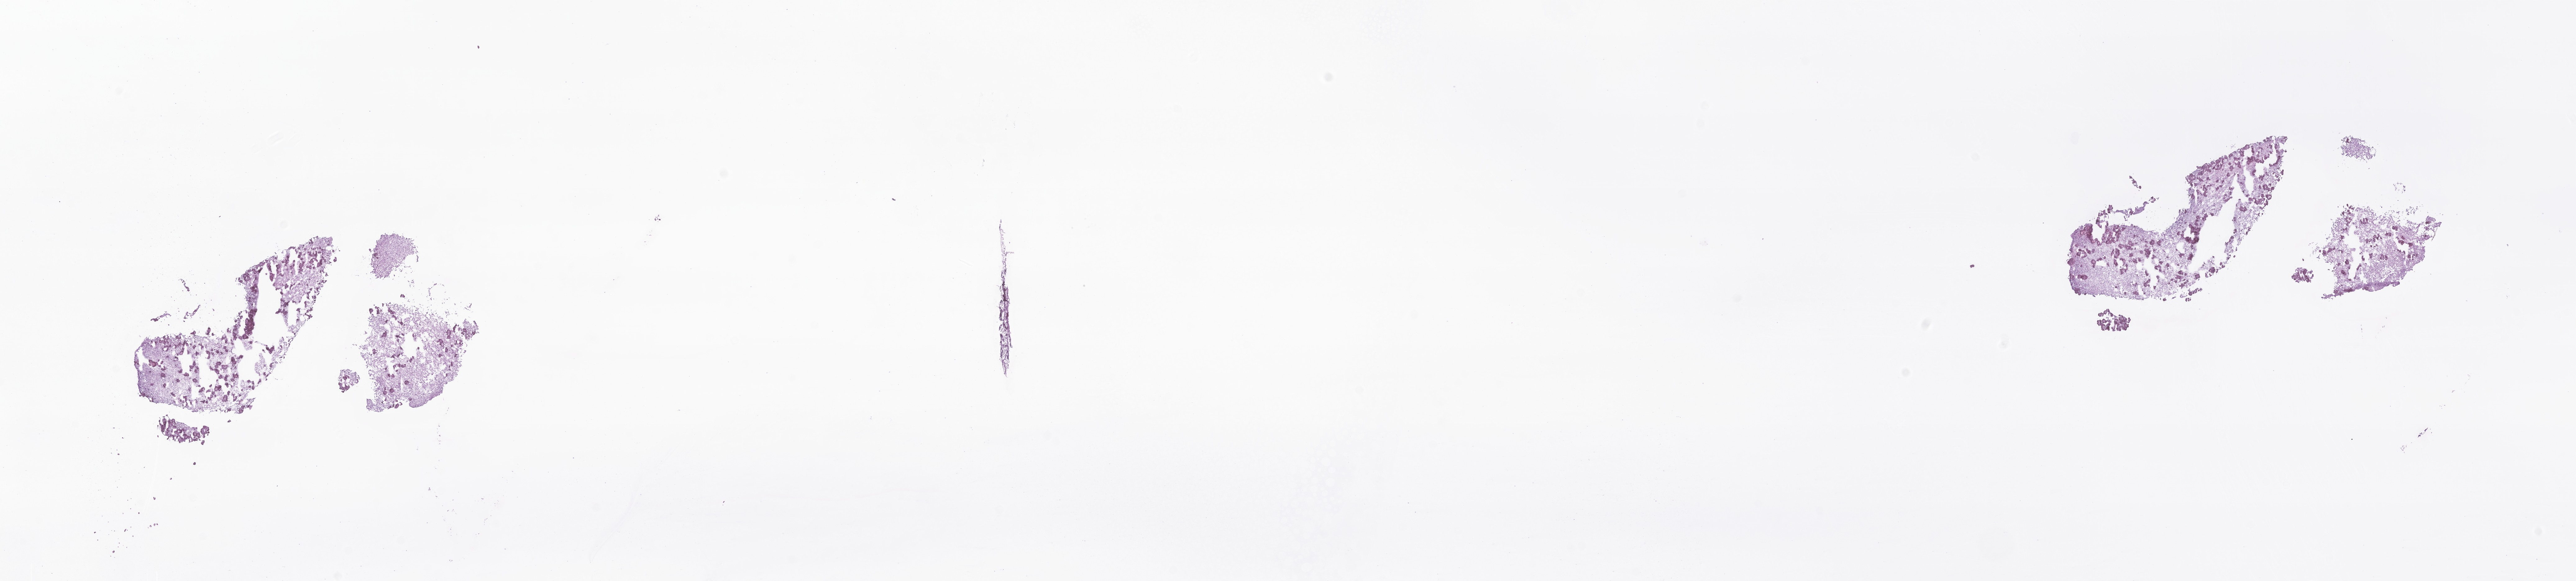
Whole-slide image, haematoxylin and eosin stain of tumor tissue from the temporal lobe — whole scanned area (about 35.0 x 7.9 mm) shown as a low-resolution overview. Frozen section. Female patient, age 209 months.
Diagnosis: Ganglioglioma, NOS.